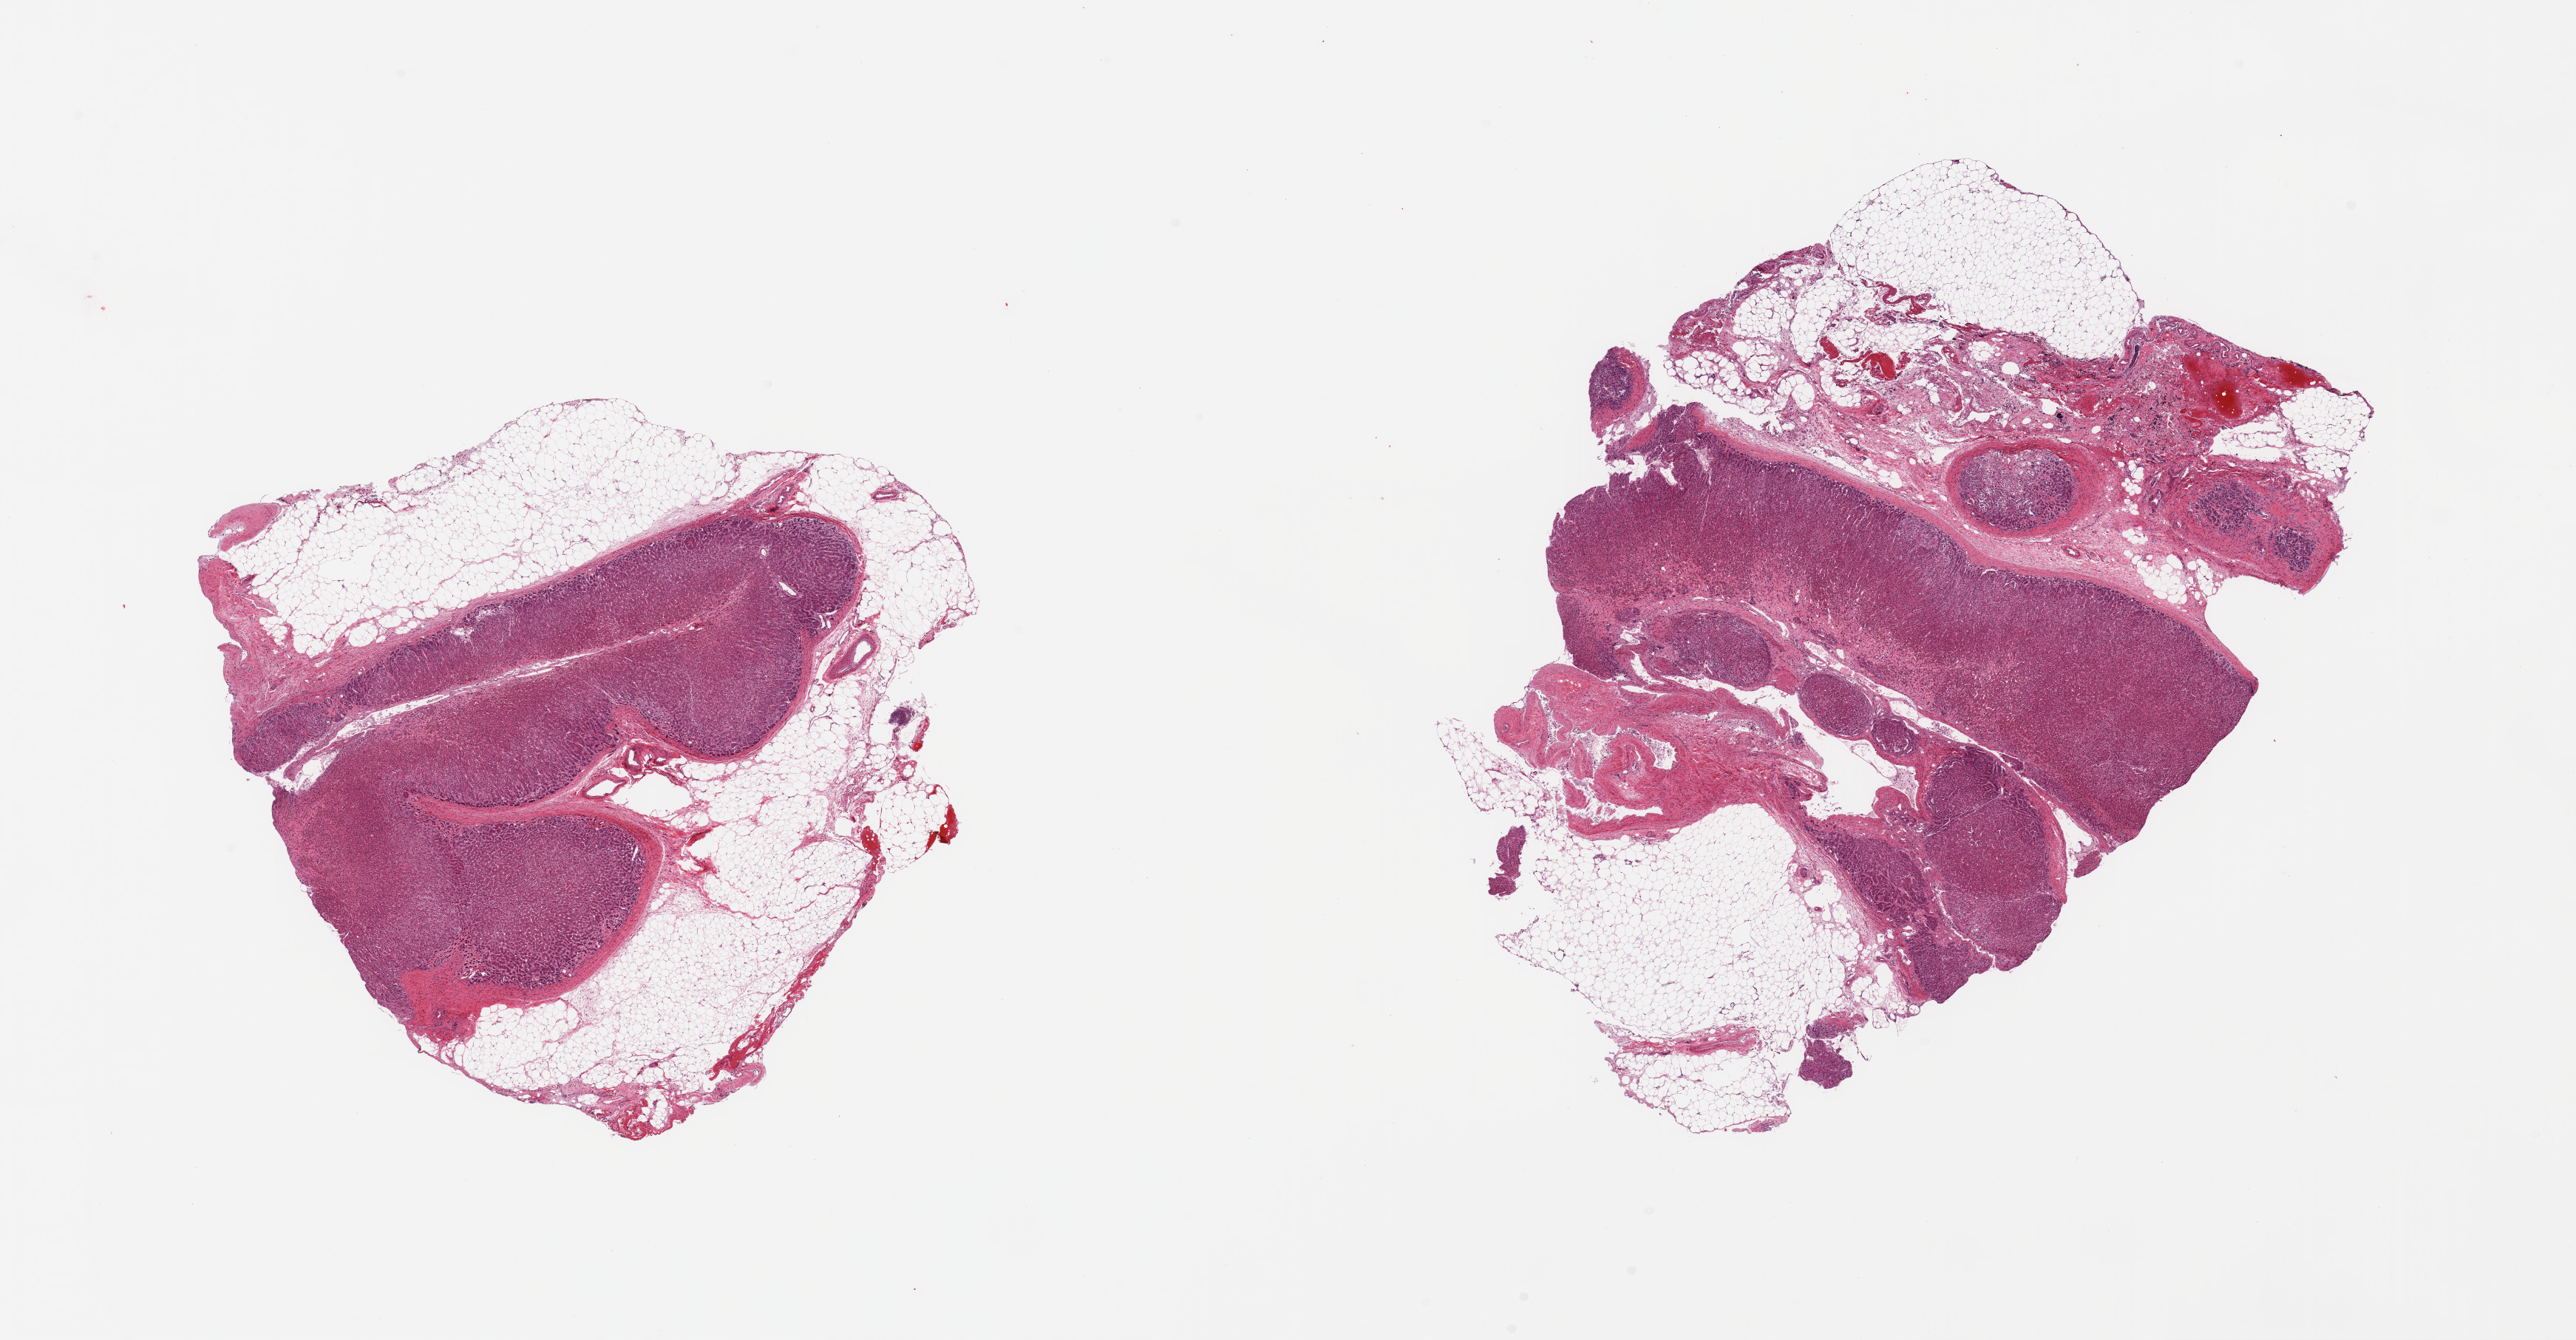
H&E whole-slide image — whole scanned area (about 27.6 x 14.3 mm, from a 20x scan) shown as a low-resolution overview, PAXgene-fixed, paraffin-embedded tissue, sampled site (target tissue): adrenal gland, donor tissue sample.
Reviewer comment on this tissue sample: 2 pieces; both include 50-60% attached fat/connective tissue with some inflammatory cells.